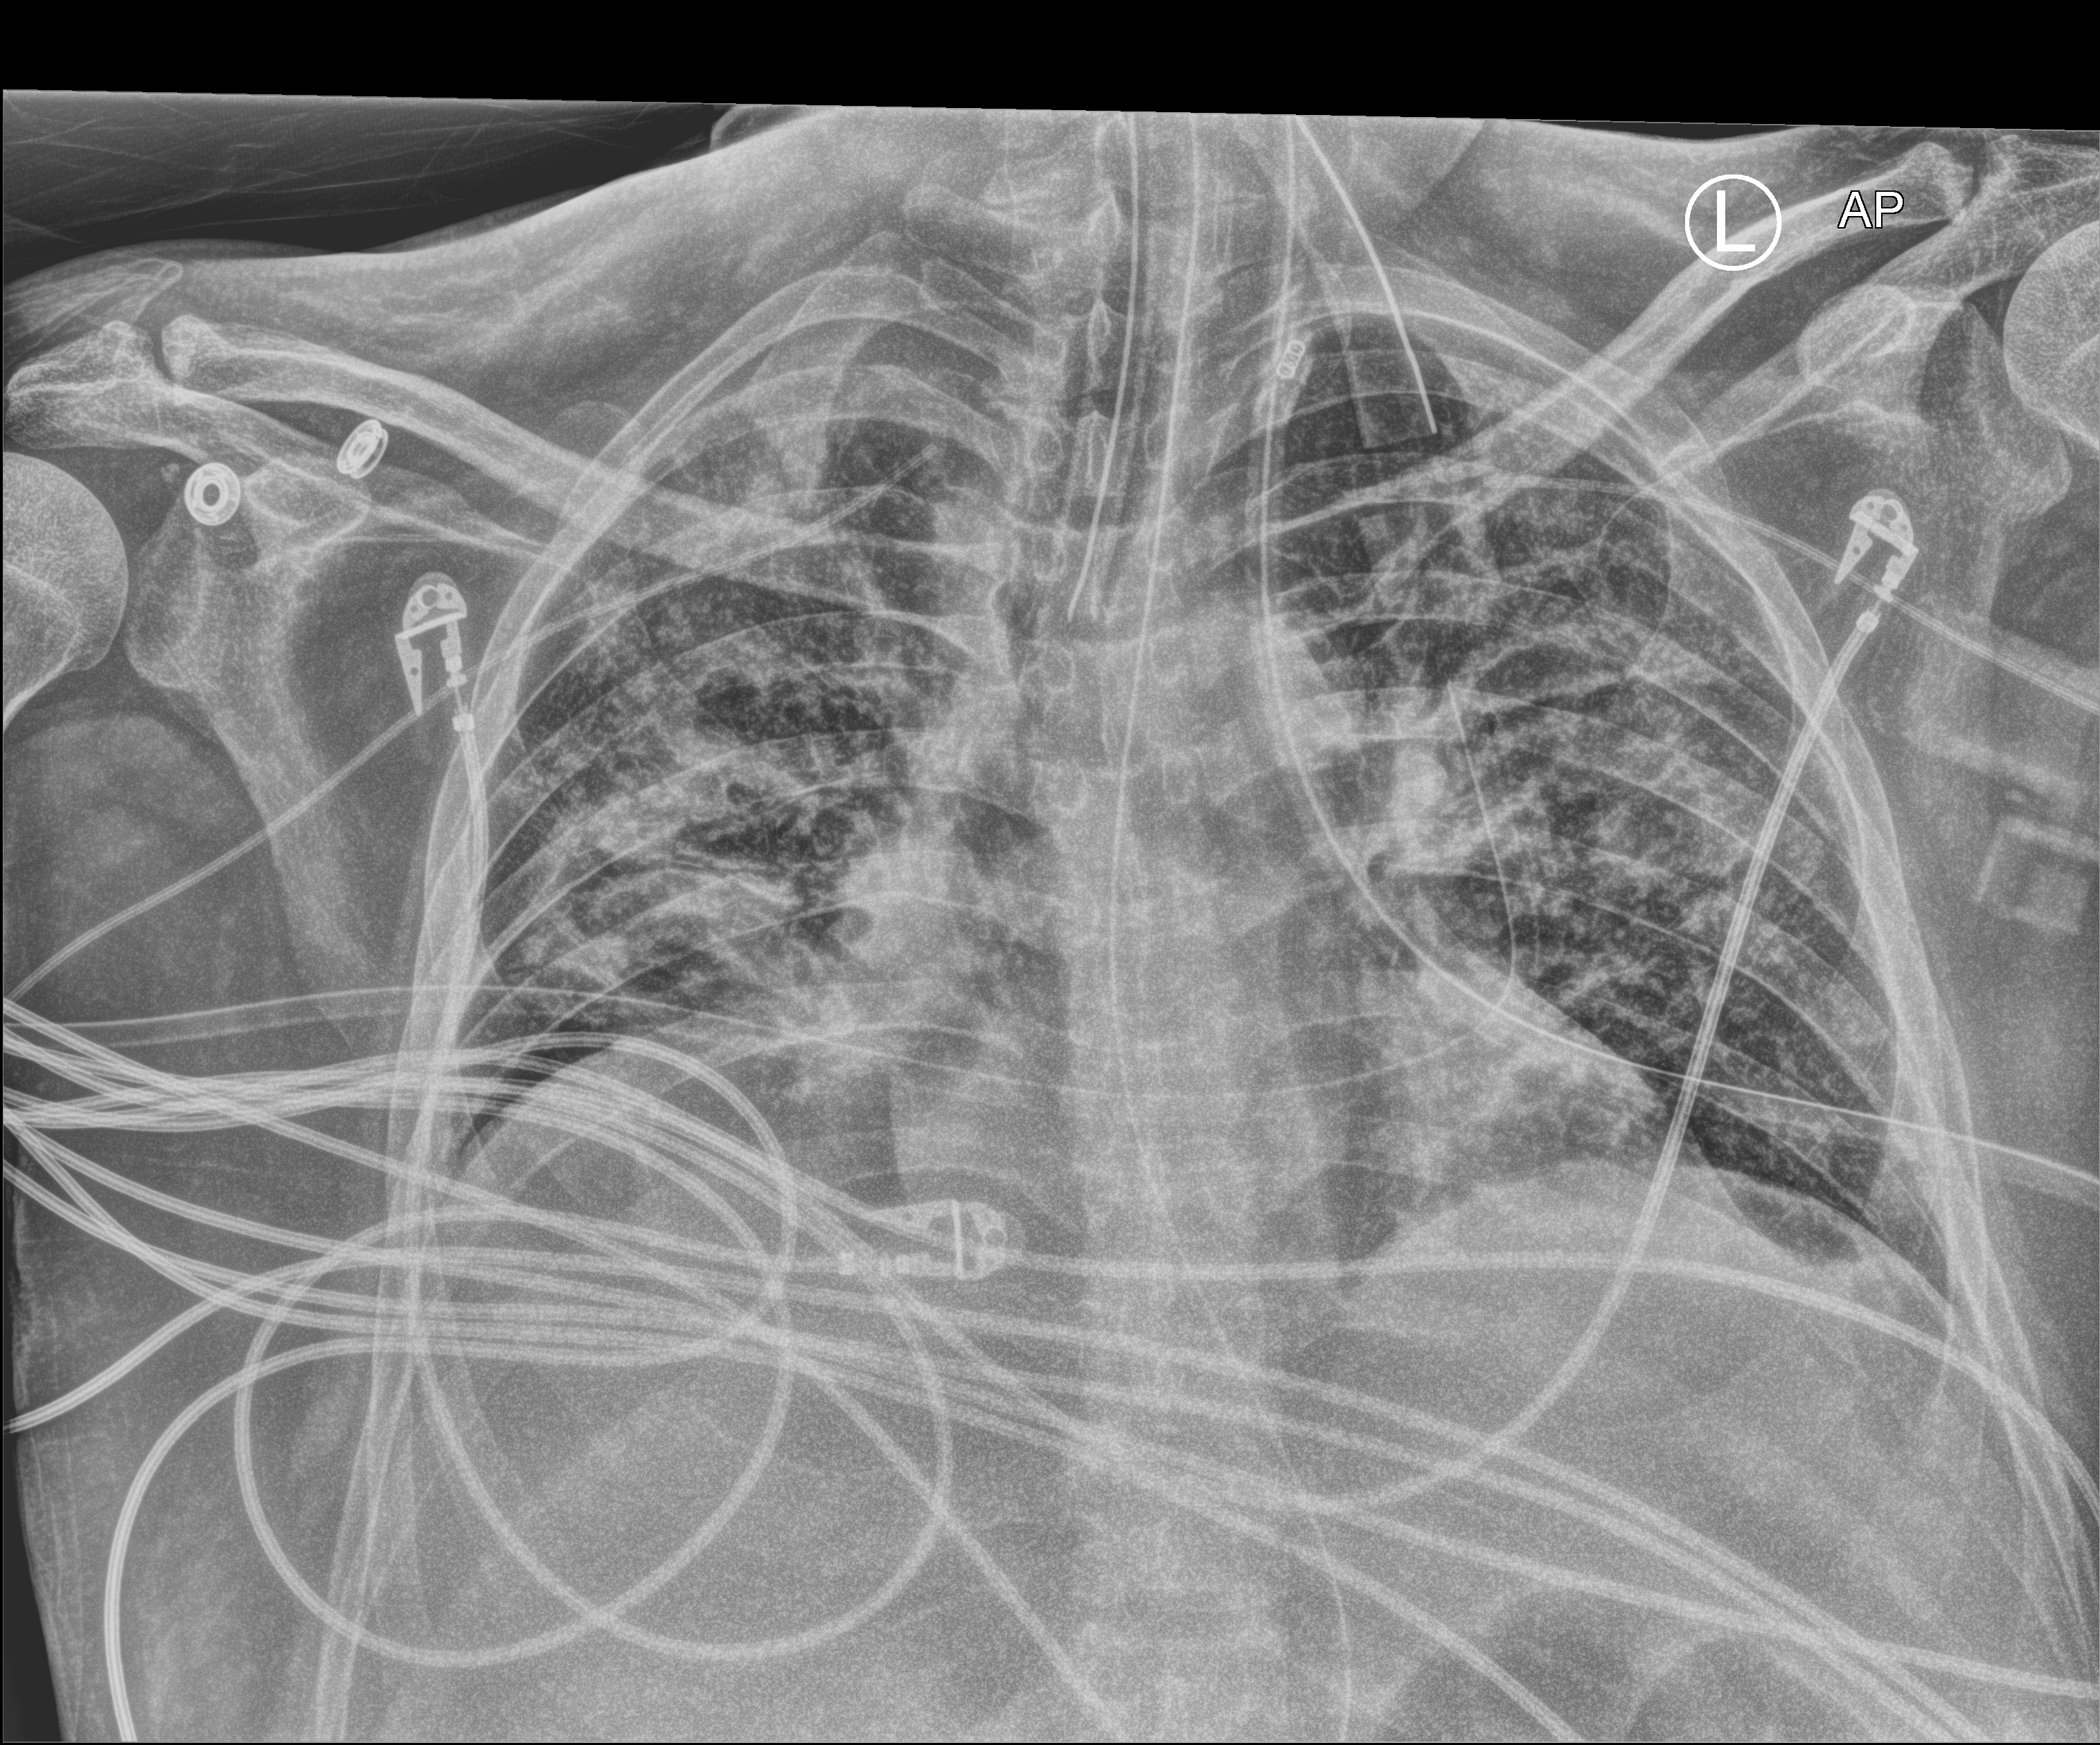
Chest X-ray (portable); anteroposterior (AP) projection. Patient hospitalised with COVID-19, aged 18–59 years.
Hospital-stay facts (about this admission, not read from this image; timing relative to this image not recorded): length of hospital stay: 50 days; admitted to intensive care during this hospital stay: yes.